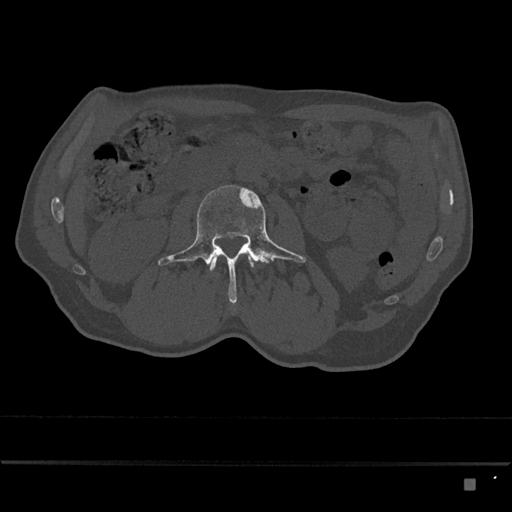
CT including the spine, one axial slice; slice 418 of 797 in the series (ordered by position); bone window (W 1800 / L 400 HU); 0.5 mm slice thickness; 512 × 512 image matrix, field of view 390 × 390 mm. Male patient, age 72 years. From the clinical record (not read from this slice): primary cancer: prostate.
Annotated regions visible in this slice (semi-automatic segmentation, software-assisted and operator-edited):
- L2 vertebra: bounding box (x1, y1, x2, y2) in pixels: (210, 255, 254, 271)
- L3 vertebra: (158, 185, 306, 305)